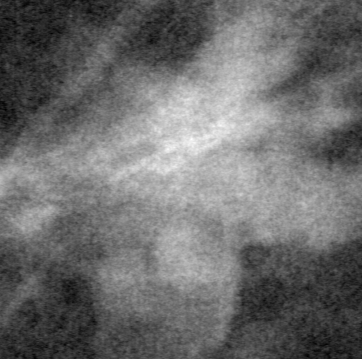
Cropped region of a digitized screen-film mammogram centred on a radiologist-marked abnormality; left breast; CC view.
- Finding: mass, shape irregular, margins ill defined; BI-RADS assessment category 4; pathology result (as recorded, not read from the image): malignant.